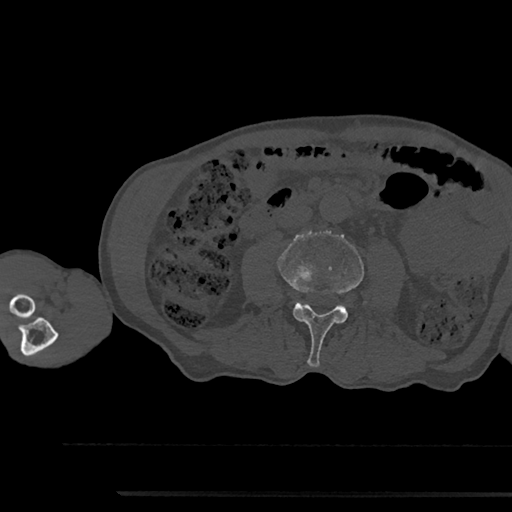
CT including the spine, one axial slice. Slice 475 of 797 in the series (ordered by position). Reconstruction kernel Br40s/3. Bone window (W 1800 / L 400 HU). 0.5 mm slice thickness. 512 × 512 image matrix, field of view 367 × 367 mm. Male patient, age 79 years. Case-level facts recorded for this patient, not image findings: primary cancer: prostate.
Outlined on this slice (semi-automatic segmentation, software-assisted and operator-edited):
- L3 vertebra: box from (x=278, y=231) to (x=364, y=367) px